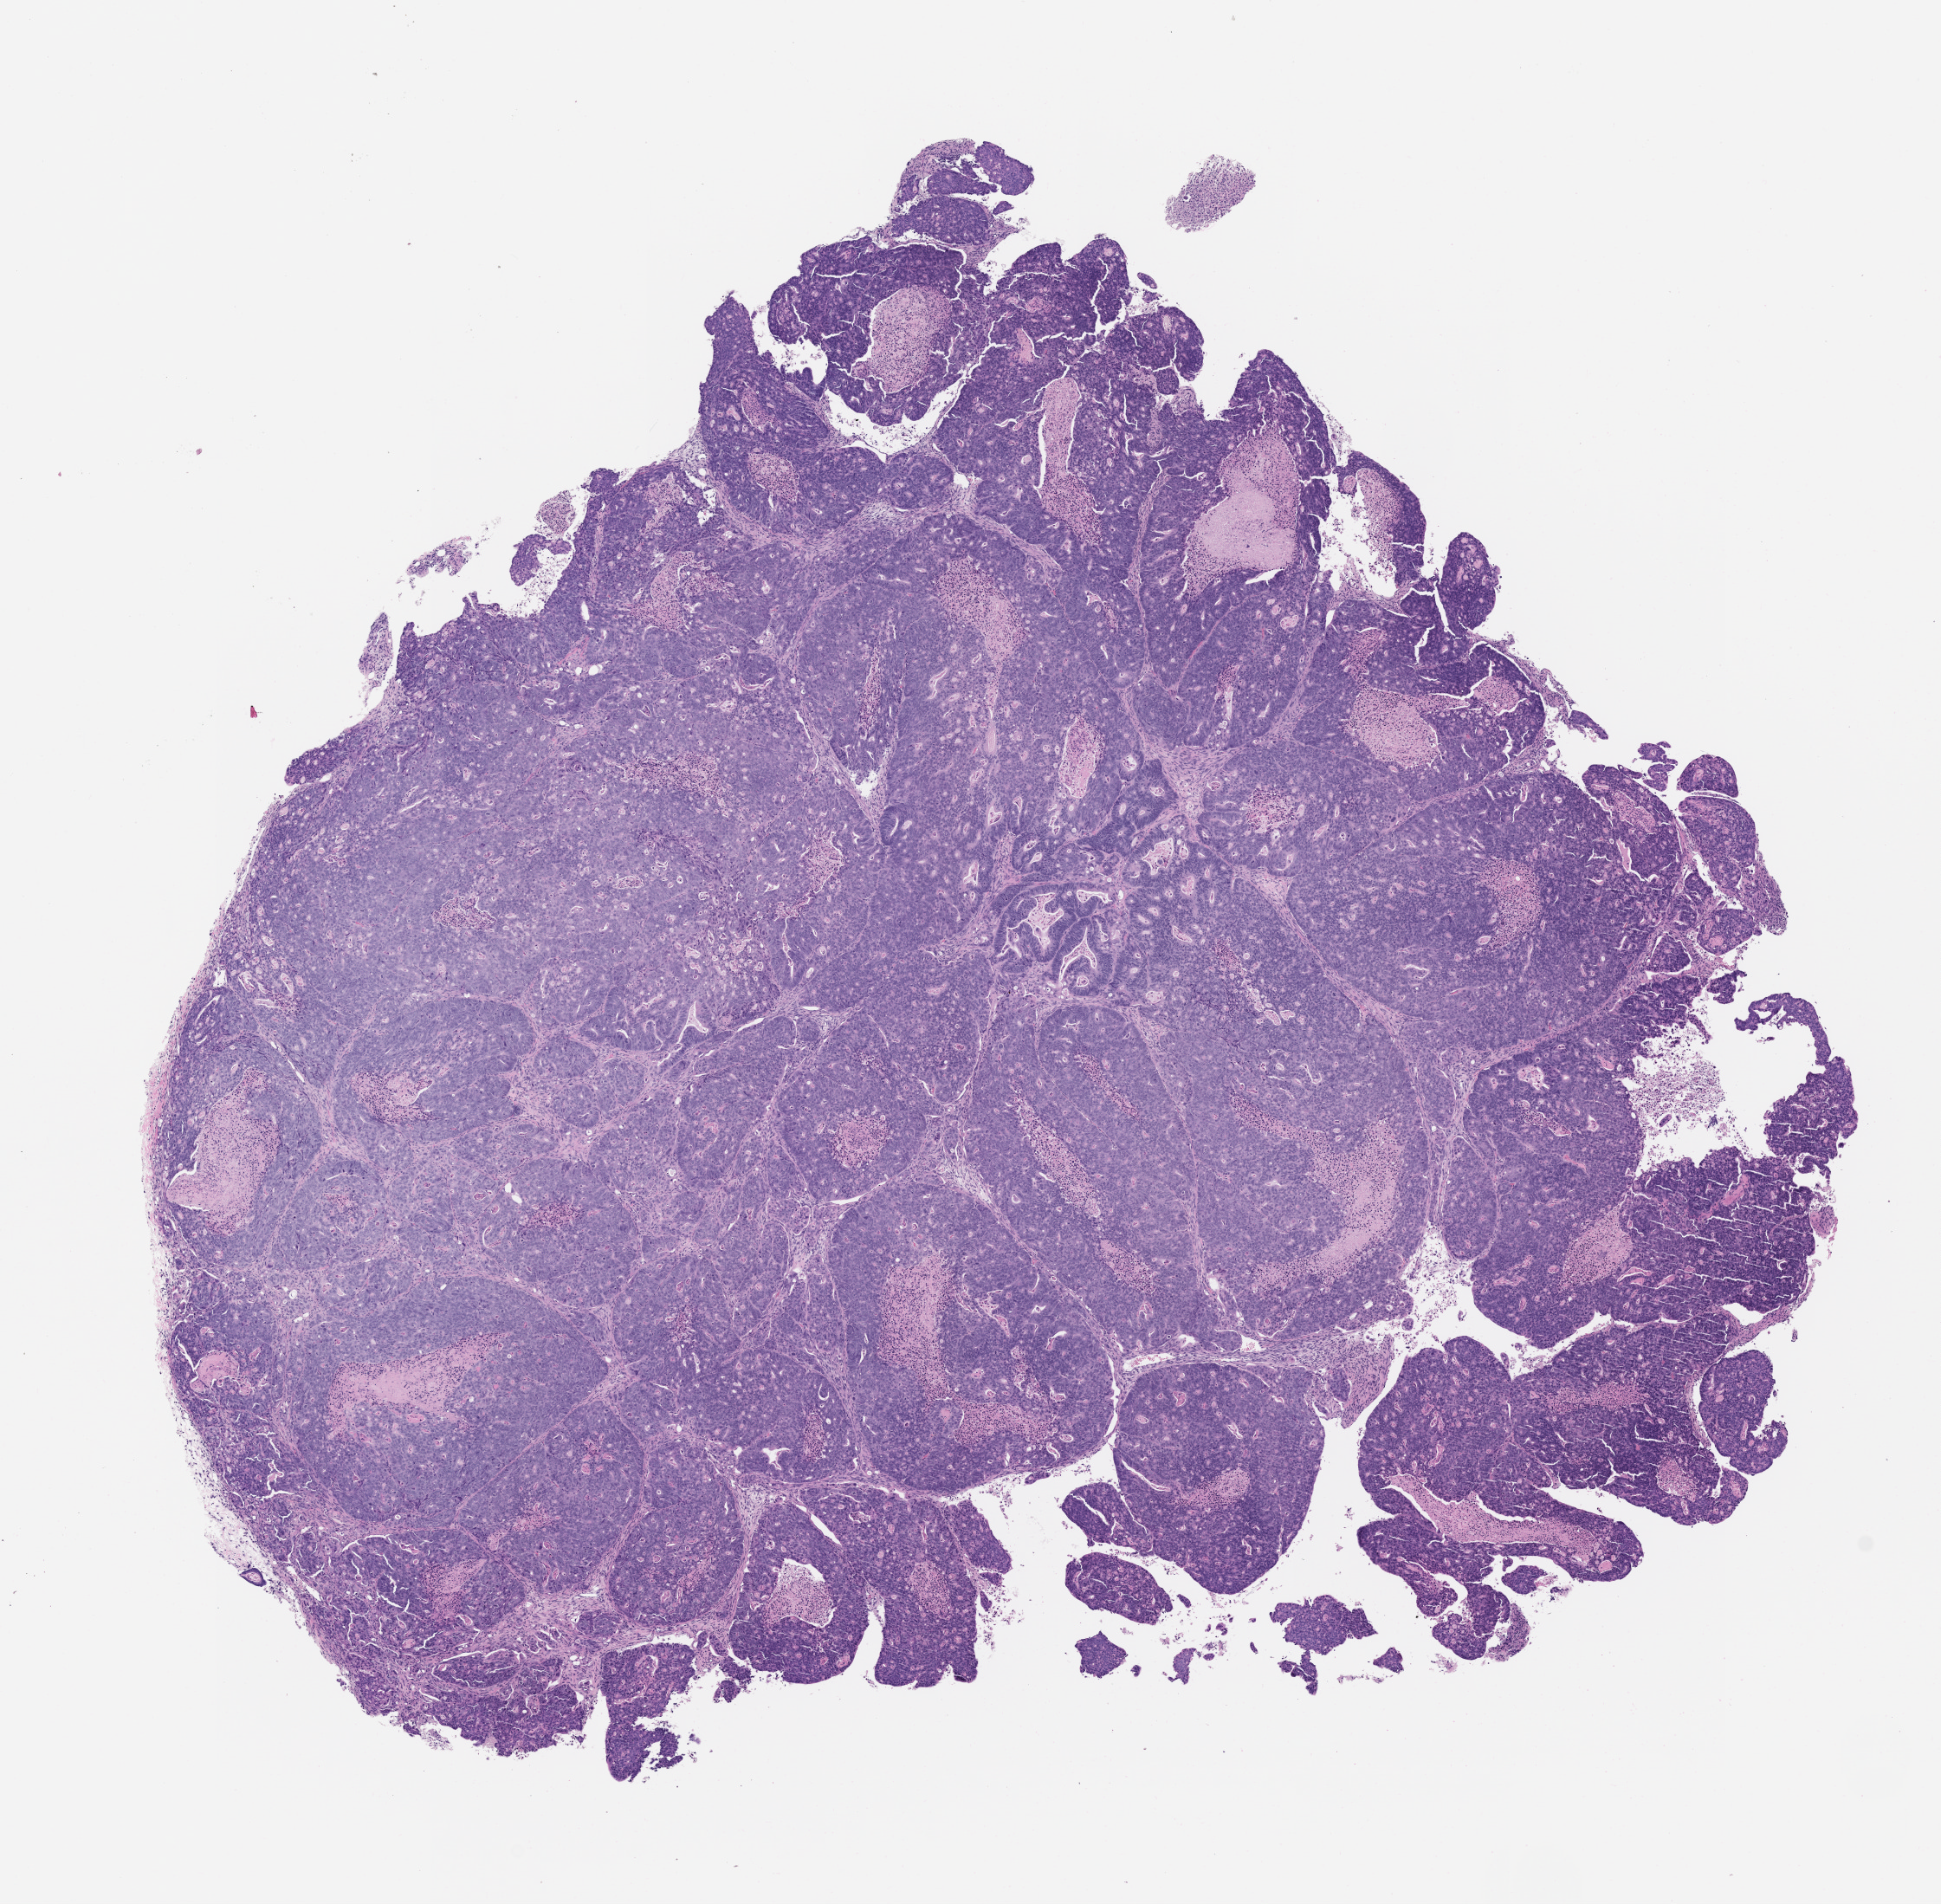
Haematoxylin and eosin whole-slide image of a patient-derived xenograft (PDX) tumor grown in a mouse, passage 1 — whole scanned area (about 9.0 x 8.8 mm) shown as a low-resolution overview; formalin-fixed, paraffin-embedded (FFPE) tissue; originating tumor site category: colon.
• originating patient diagnosis: Colon Adenocarcinoma